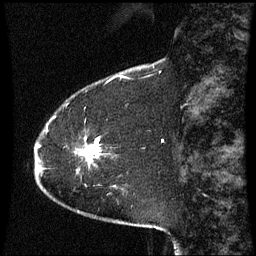
Breast MRI (dynamic contrast-enhanced), one sagittal slice. Position 11 of 60 along the scan axis. Dynamic contrast-enhanced series, image 2 of 3 at this slice position (ordered by acquisition). 1.5 T. TE 4.2 ms, TR 8.9 ms. 256 × 256 image matrix. Patient: female, 51 years. From the clinical record (not read from this slice): setting: breast cancer imaged before/during neoadjuvant chemotherapy; receptor status: HR-positive, HER2-negative.
Outlined on this slice (semi-automatically segmented with operator editing):
- analysis volume of interest (the breast-tissue region the enhancement analysis was run in; not a lesion): box from (x=54, y=120) to (x=100, y=174) px
- tumour enhancement mask (voxels above the 70 % enhancement threshold inside the analysis volume of interest): (x=83, y=141)–(x=99, y=160)